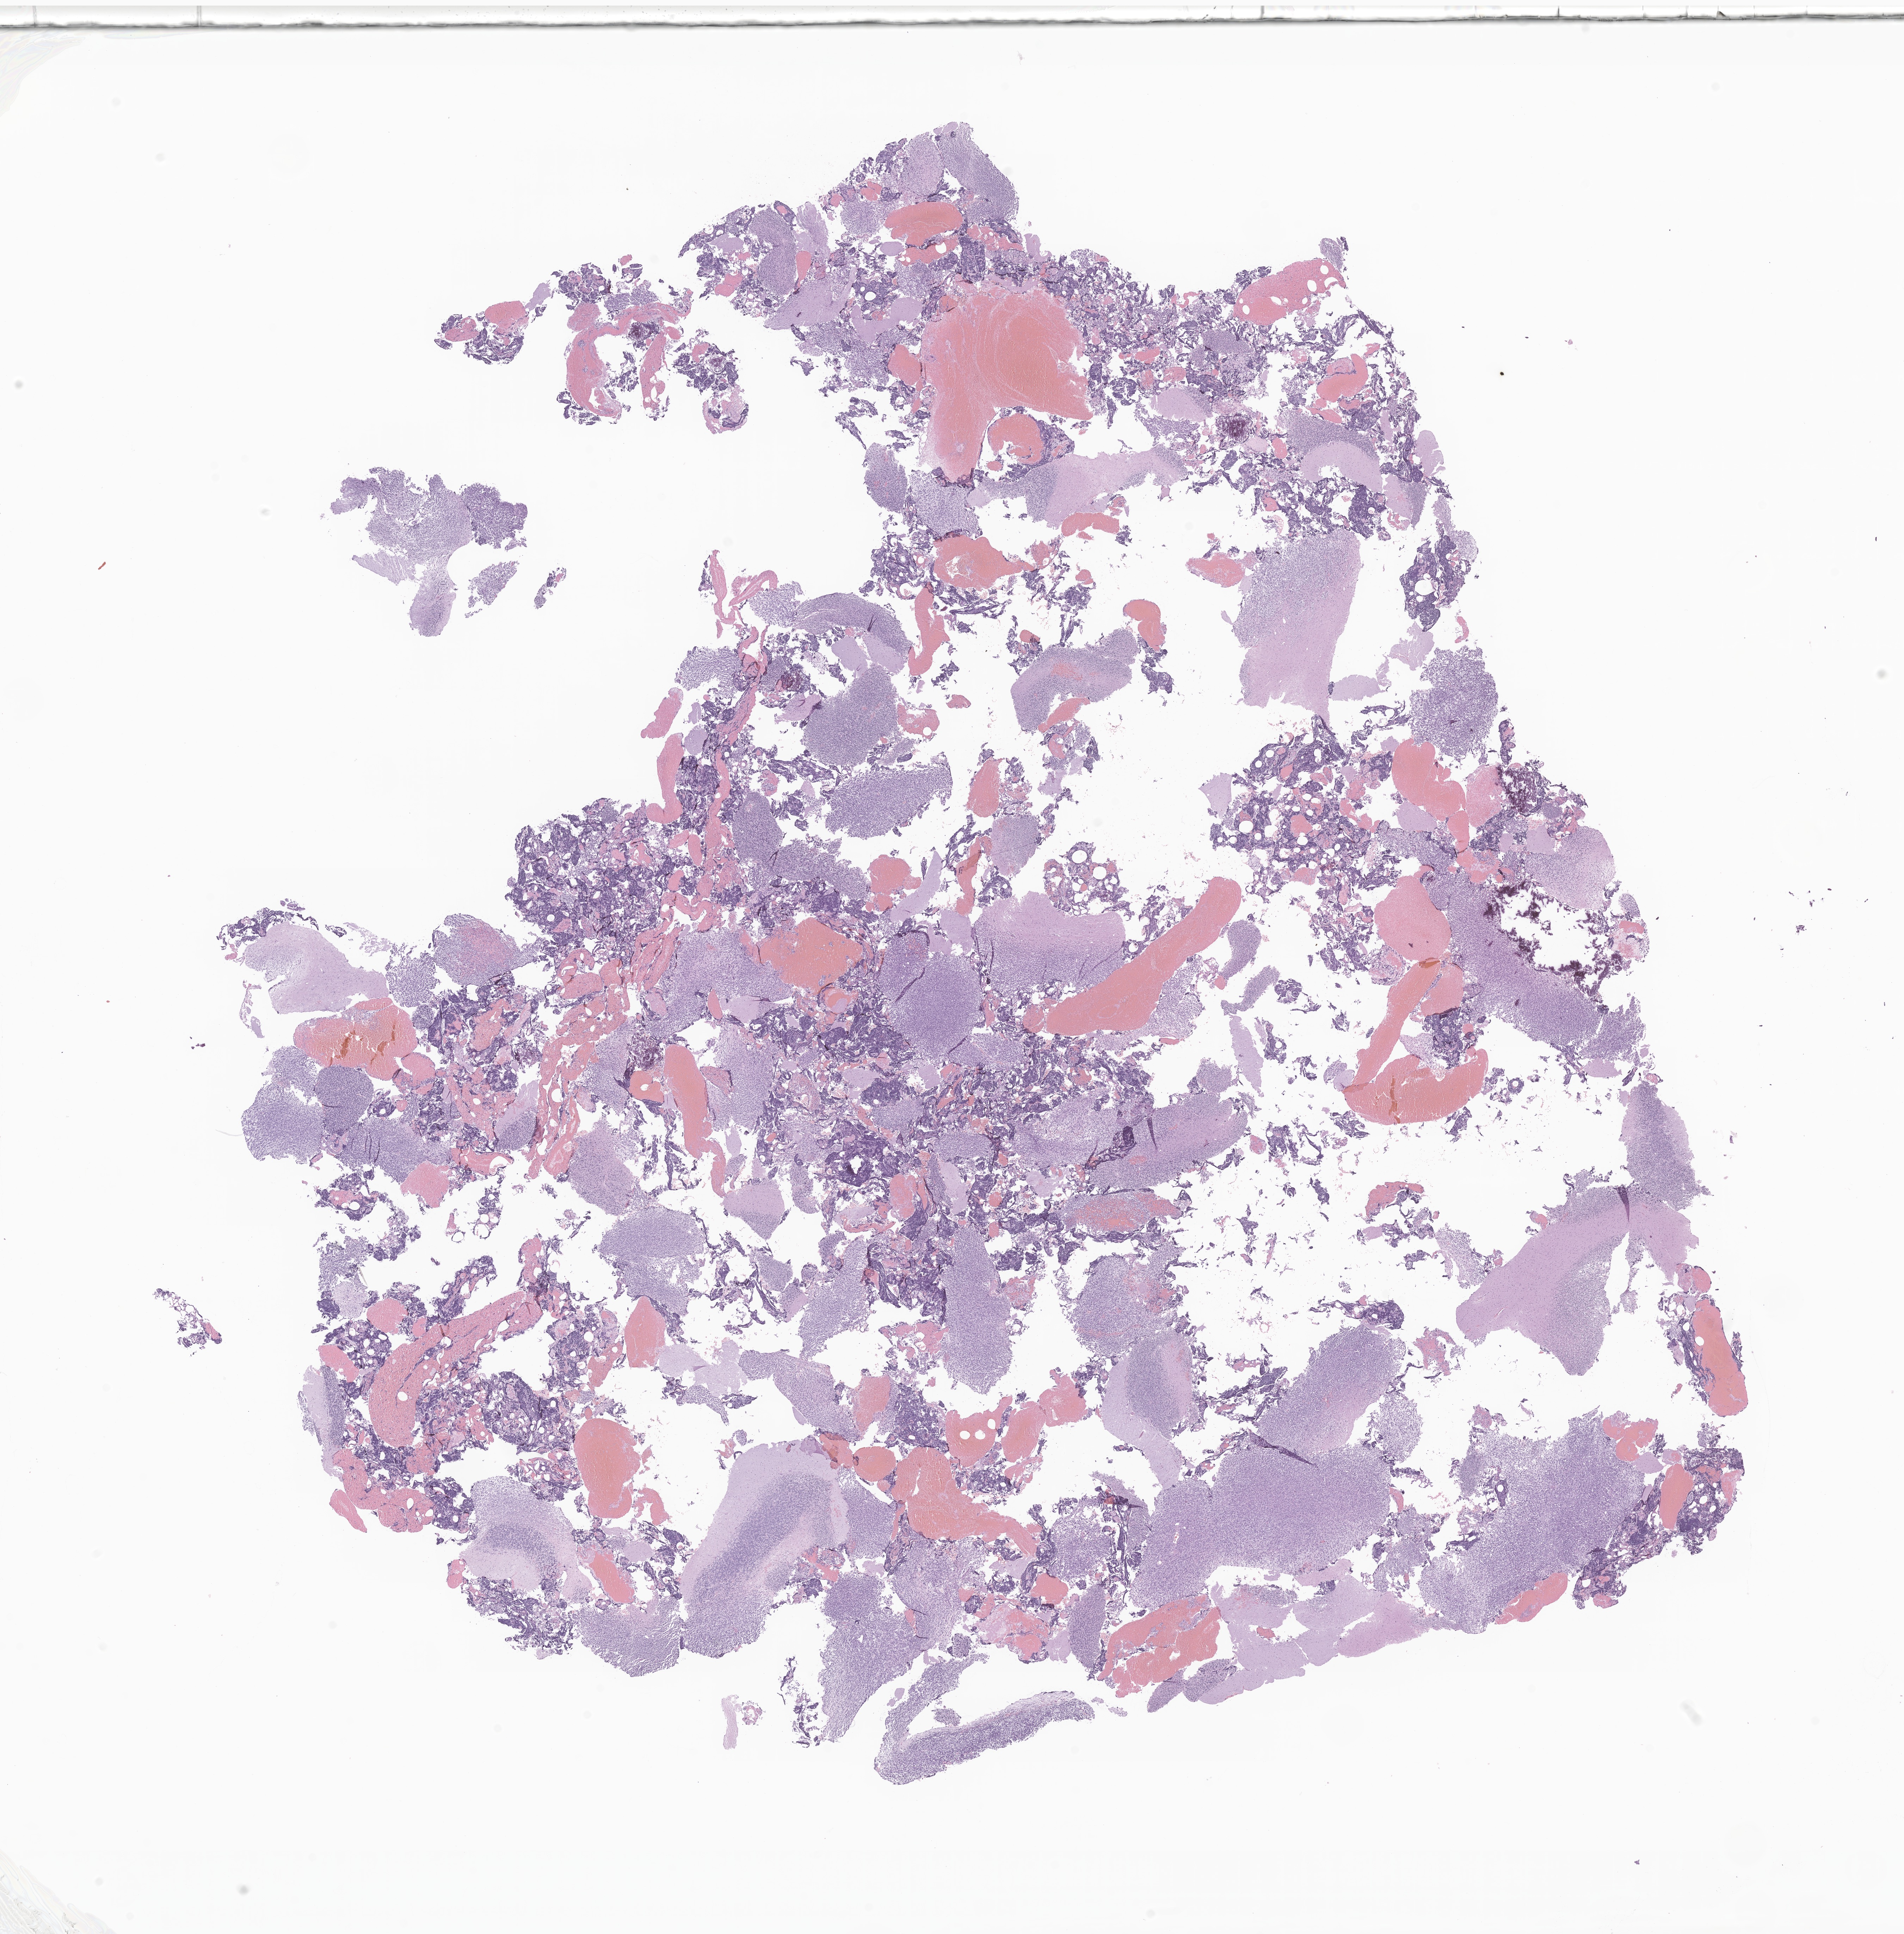
Haematoxylin and eosin whole-slide image of tumor tissue from the brain, a low-resolution overview of the entire scanned area, about 22.8 x 23.1 mm, formalin-fixed paraffin-embedded section. Patient: male, age 121 months (10 years 1 month).
• diagnosis: Medulloblastoma, NOS